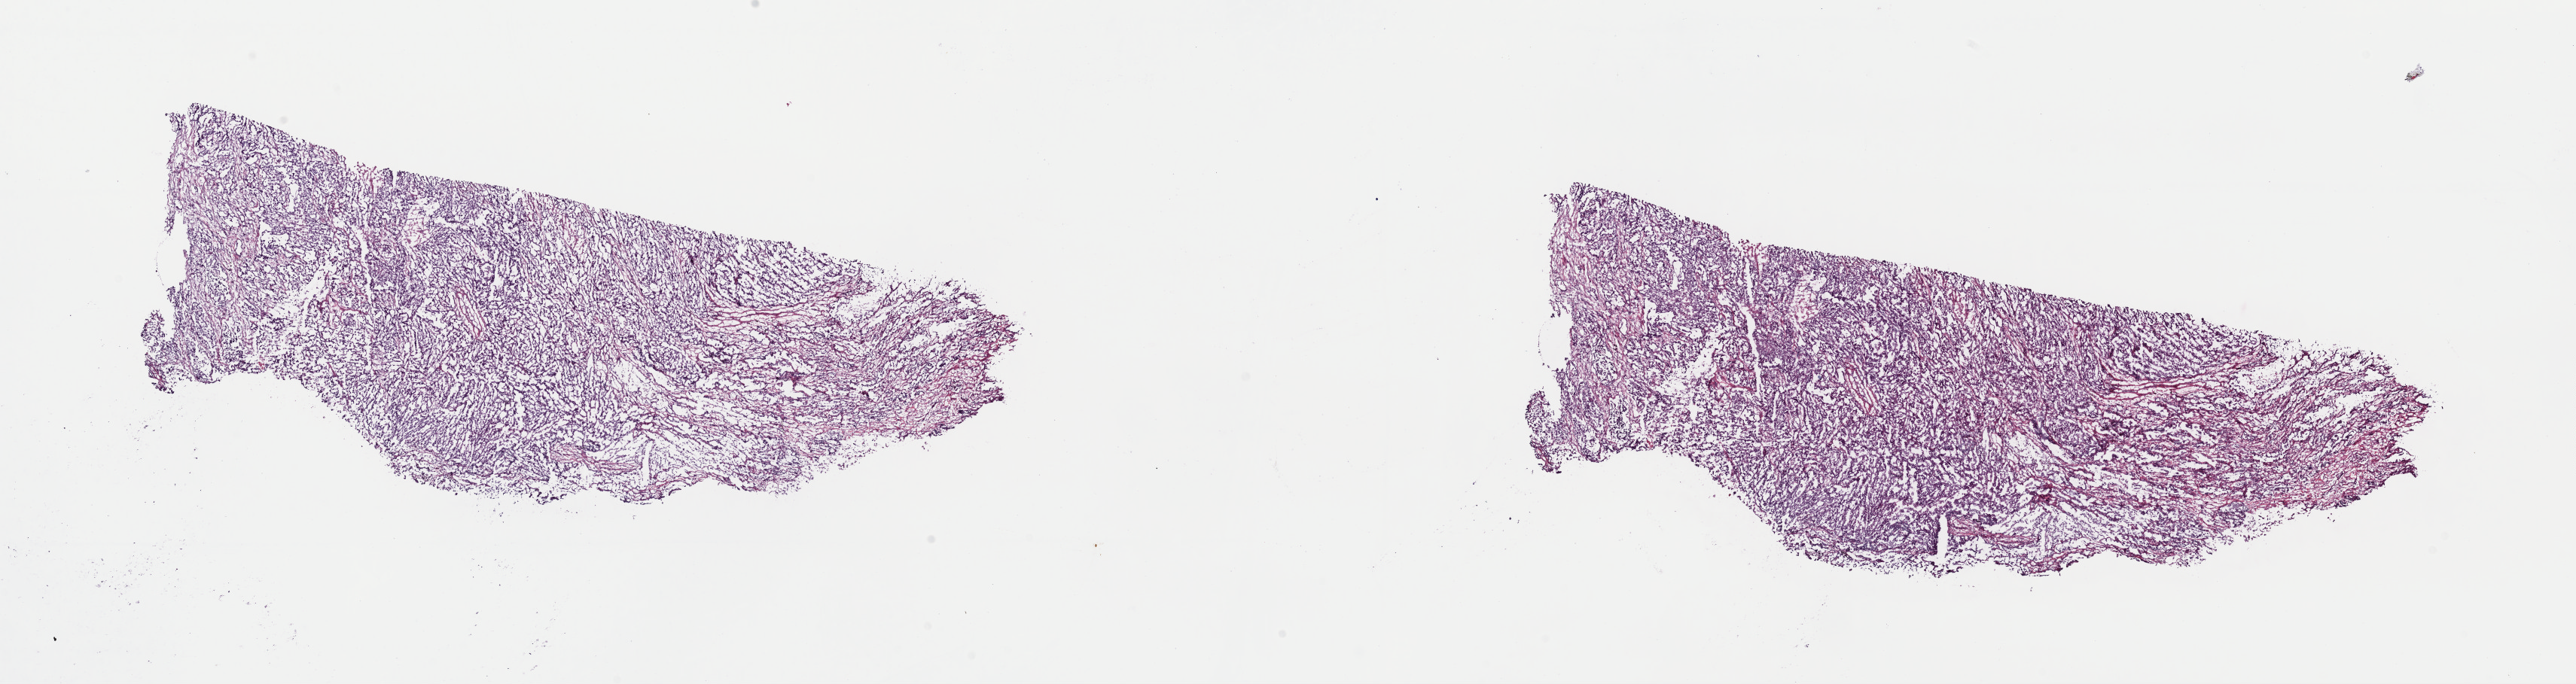
Hematoxylin and eosin (H&E) stained whole-slide image — a low-resolution overview of the entire scanned area, about 27.0 x 7.2 mm (acquisition: 40x scan); frozen section from the top of the tissue portion; primary tumour sample from the lung. Patient: male, age at initial diagnosis 56 years. Pathologist review of this section (percent, as recorded): tumour cells 95%, tumour nuclei 90%, normal cells 0%, stromal cells 0%, necrosis 5%. Infiltration values recorded for this section: lymphocyte infiltration 0%, monocyte infiltration 0%, neutrophil infiltration 0%.
Pathologic diagnosis: Adenocarcinoma, NOS (upper lobe, lung). AJCC pathologic stage: IIB.